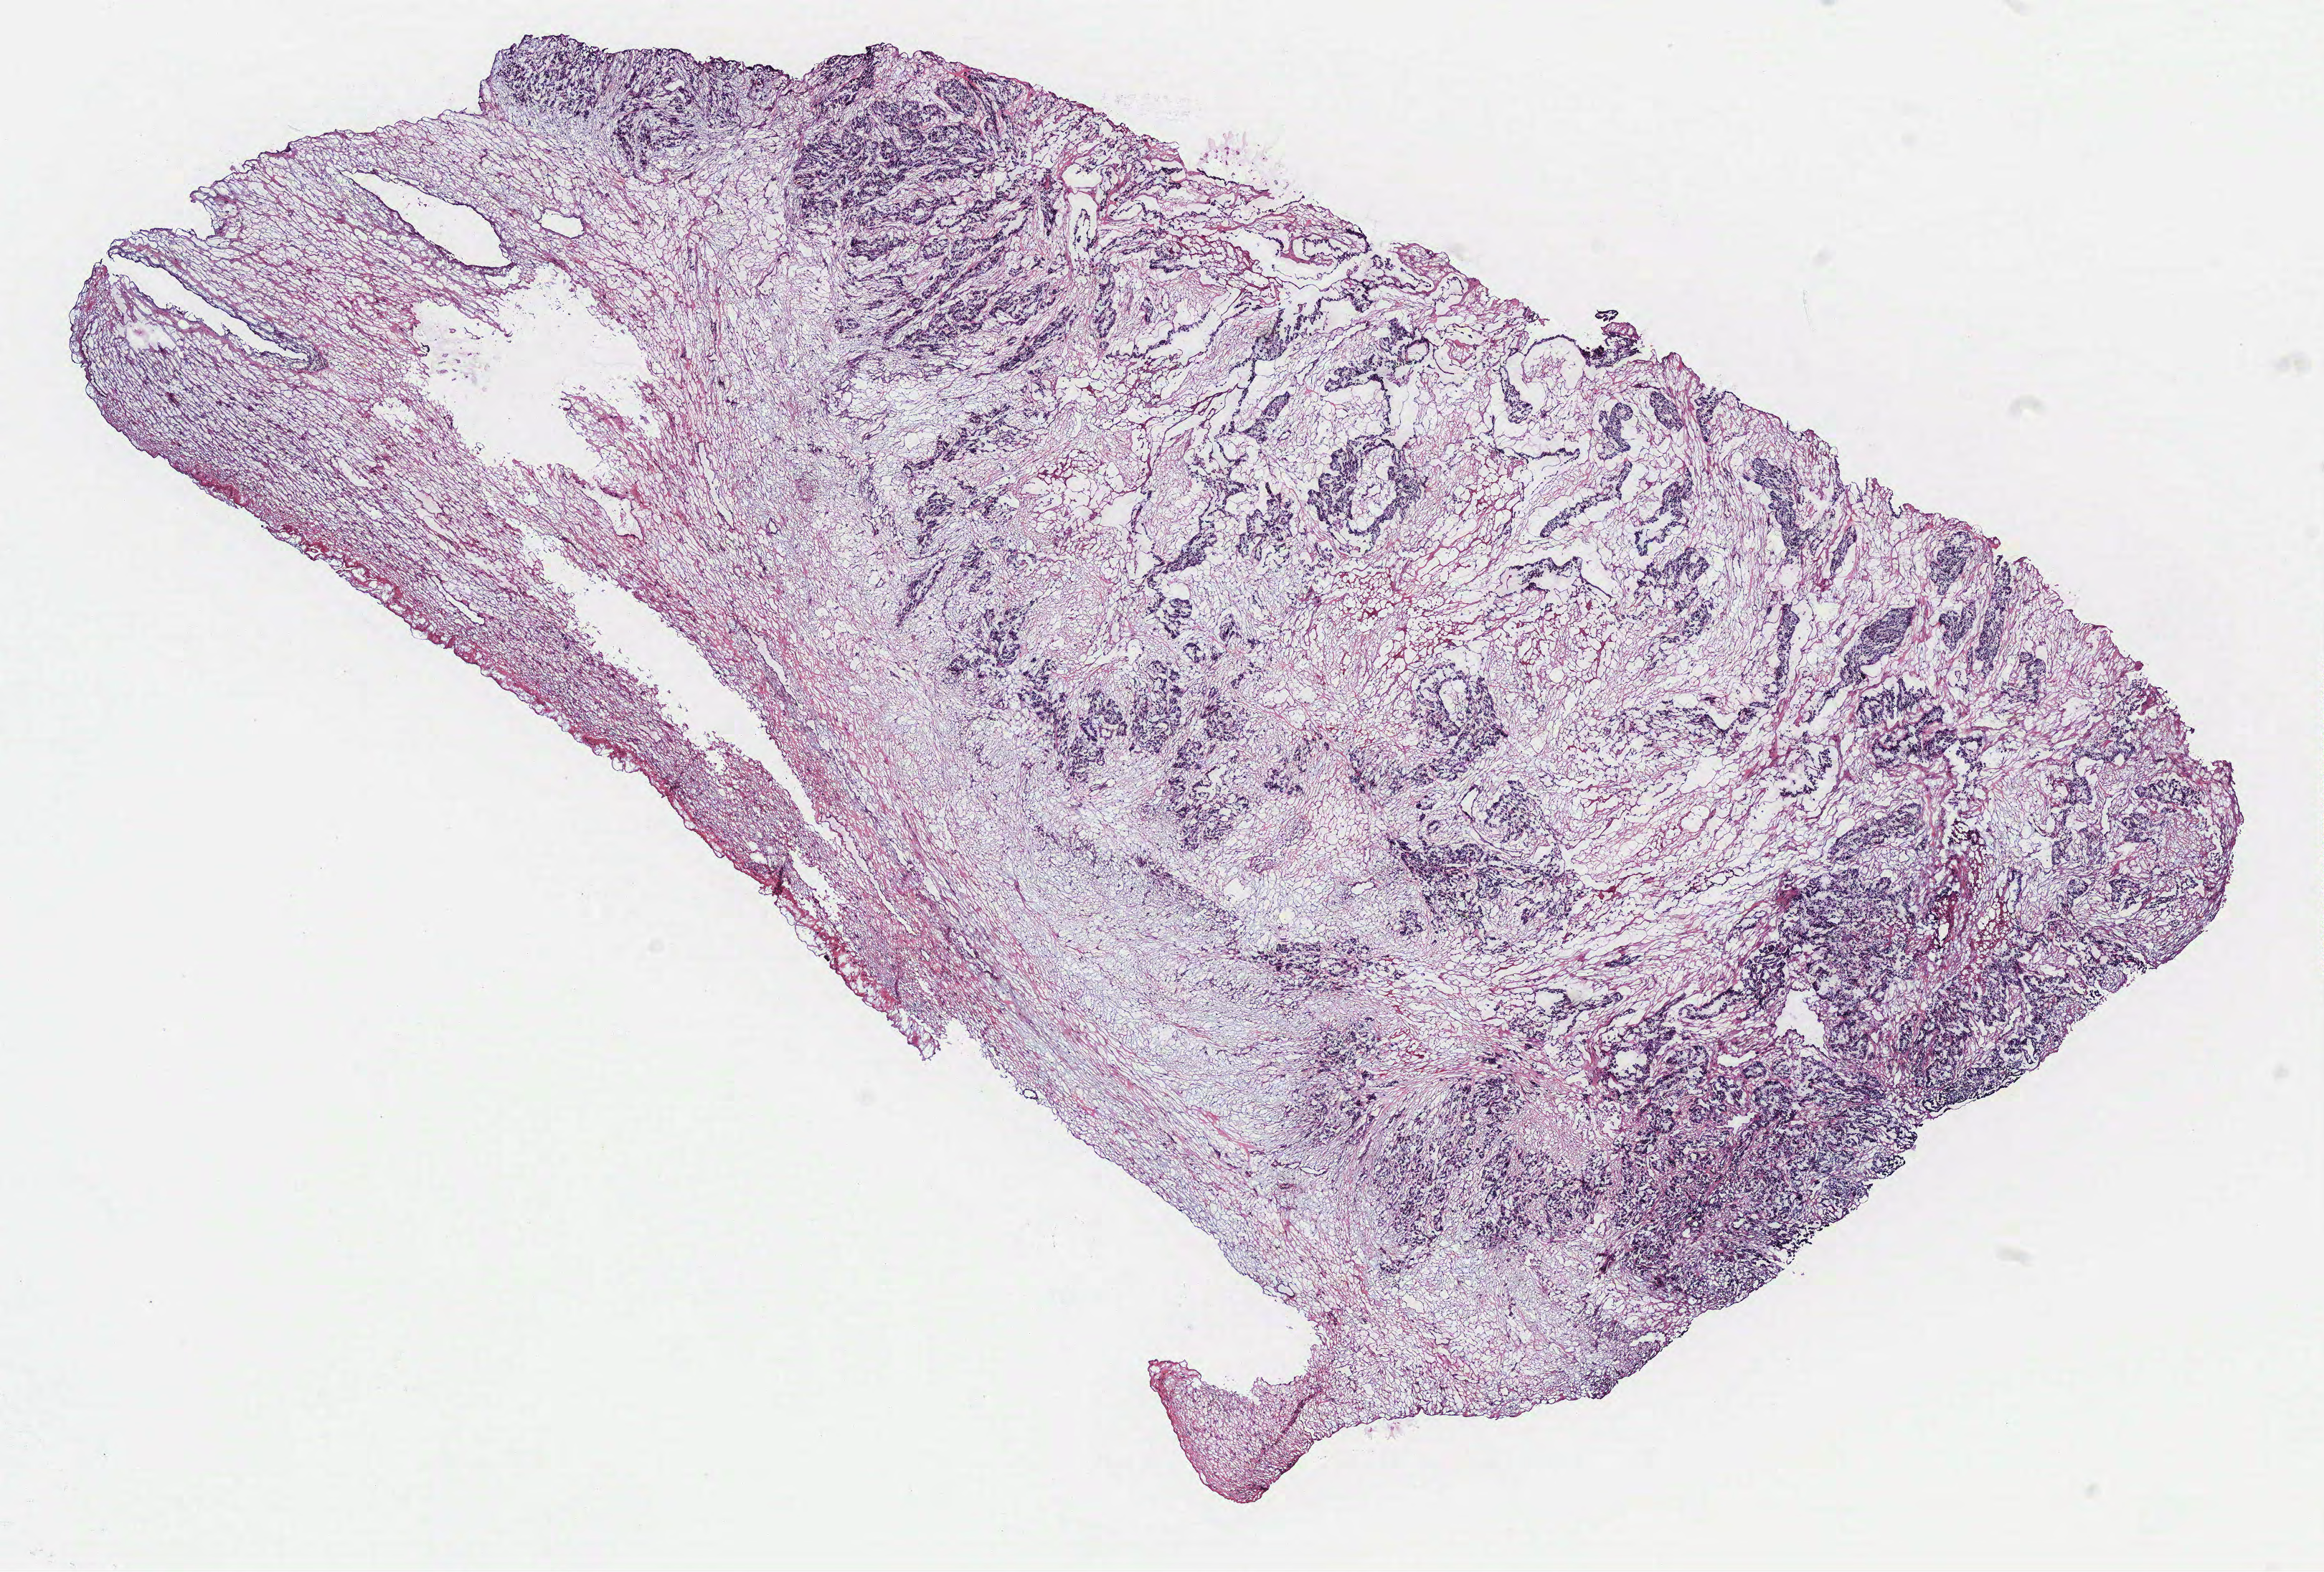
Digitized H&E-stained tissue section (whole slide) — a low-resolution overview of the entire scanned area, about 13.0 x 8.8 mm (slide scanned at 40x); normal (non-tumour) tissue sample, ovary. 58-year-old female patient.
This section: normal (non-tumour) tissue from the same patient. Patient diagnosis: Serous adenocarcinoma, NOS (peritoneum, NOS).